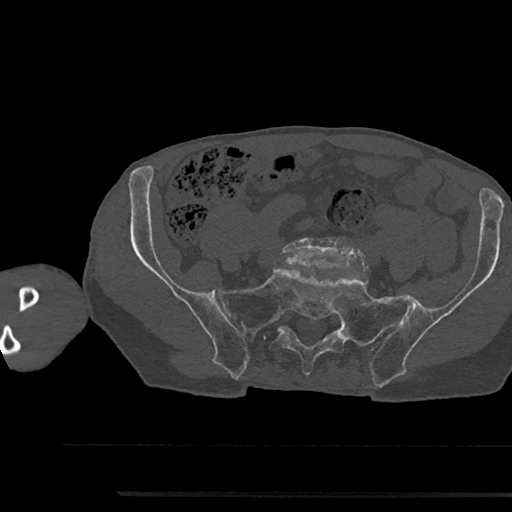
CT including the spine, one axial slice; slice 294 of 797 in the series (ordered by position); reconstruction kernel Br40s/3; 120 kVp; bone window (W 1800 / L 400 HU); 512 × 512 image matrix. Male patient, age 79 years. From the clinical record (not read from this slice): primary cancer: prostate.
Annotated regions visible in this slice (semi-automatically segmented with operator editing):
- L5 vertebra: bounding box [x1, y1, x2, y2] px = [282, 237, 362, 270]